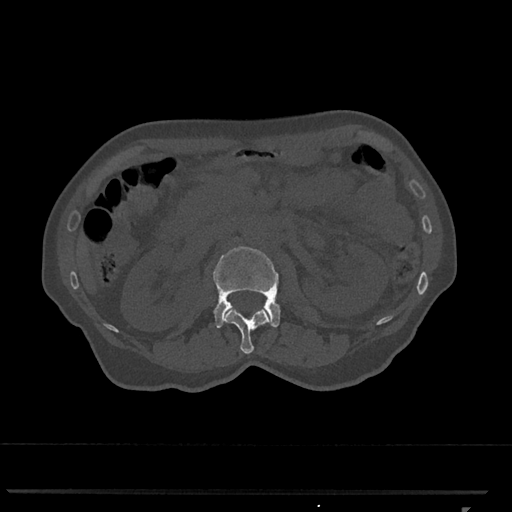
CT including the spine, one axial slice; slice 367 of 793 in the series (ordered by position); 120 kVp; bone window (W 1800 / L 400 HU); 0.5 mm slice thickness; 512 × 512 image matrix, field of view 380 × 380 mm. Patient: female, 62 years. Case-level facts recorded for this patient, not image findings: primary cancer: renal.
Structures marked on this image (semi-automatic segmentation, software-assisted and operator-edited):
- L1 vertebra: bounding box <222,307,271,354> (left, top, right, bottom; pixels)
- L2 vertebra: <213,246,281,328>